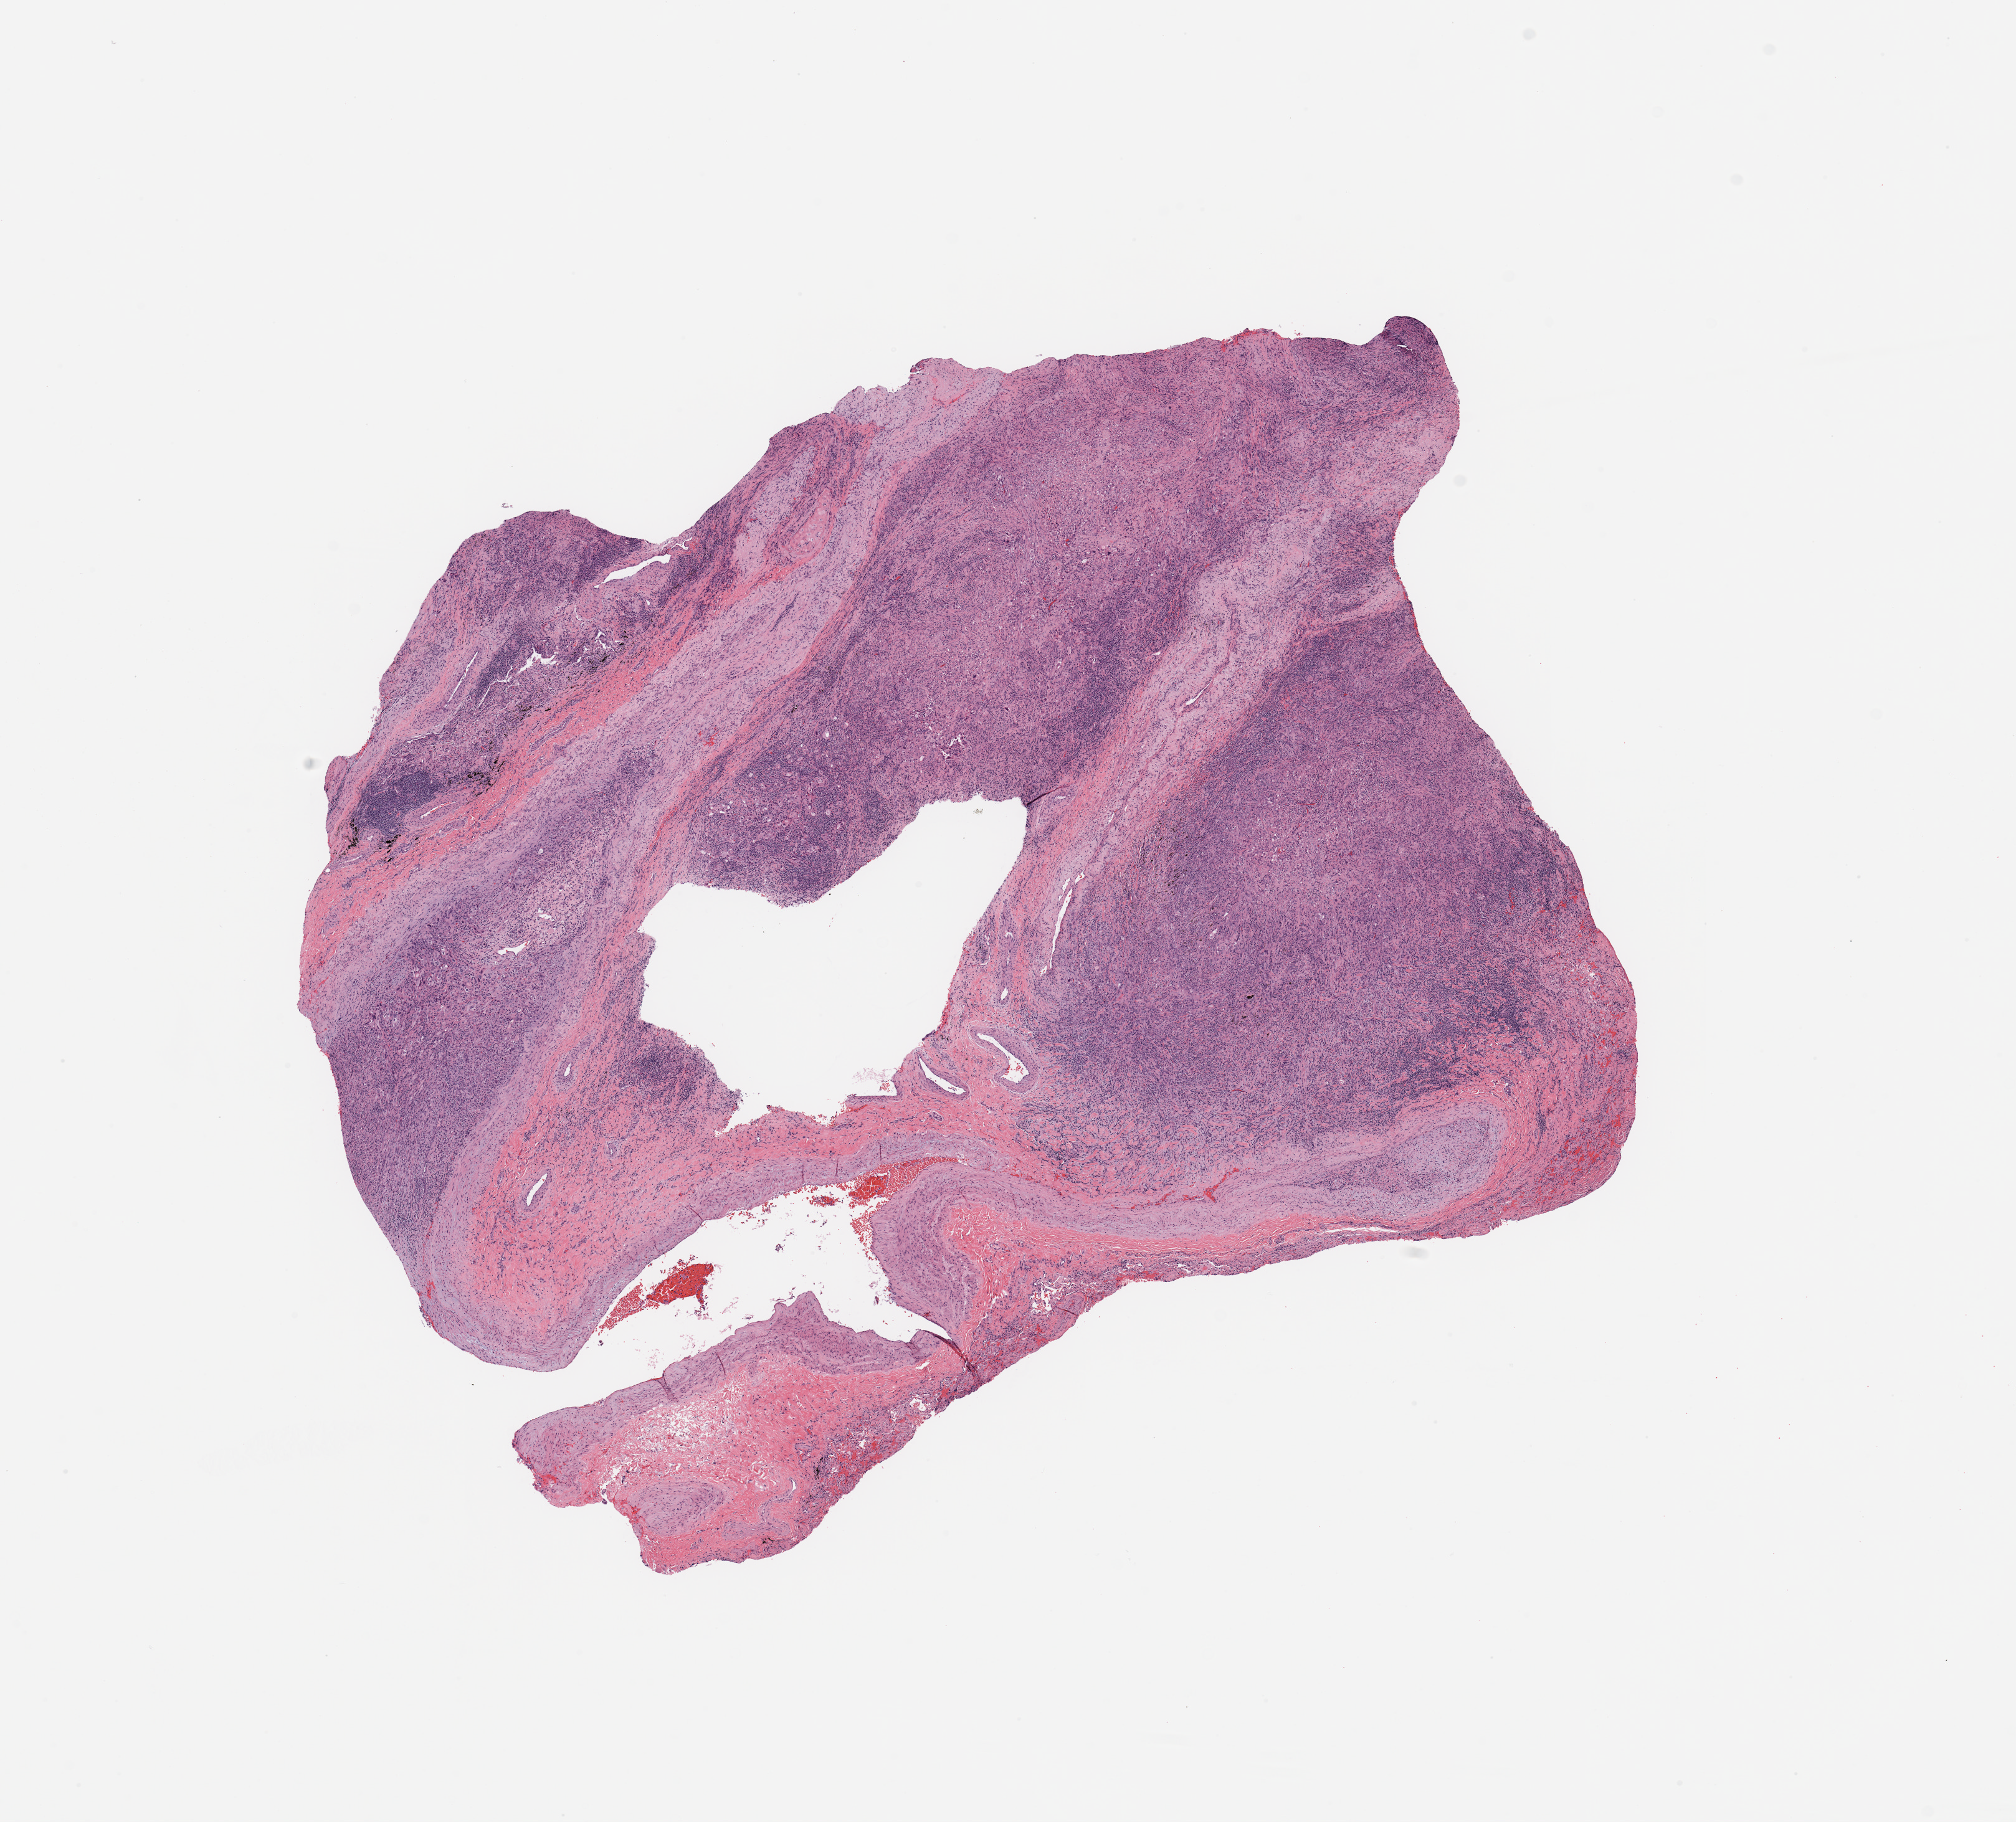
Digitized Hematoxylin and eosin (H&E) stained tissue section (whole slide) — shown as a low-resolution overview of the whole scanned area (about 12.8 x 11.6 mm, from a 20x scan). Tumour tissue sample, sampled site: lung. Patient: male, age 77 years. Histologic grade: G3 (poorly differentiated). Composition of this section per pathologist review: tumour nuclei 60%, necrosis 3%.
Primary tumour site (as recorded): right lower lobe. AJCC pathologic stage: IB. Diagnosis: Adenocarcinoma, NOS.